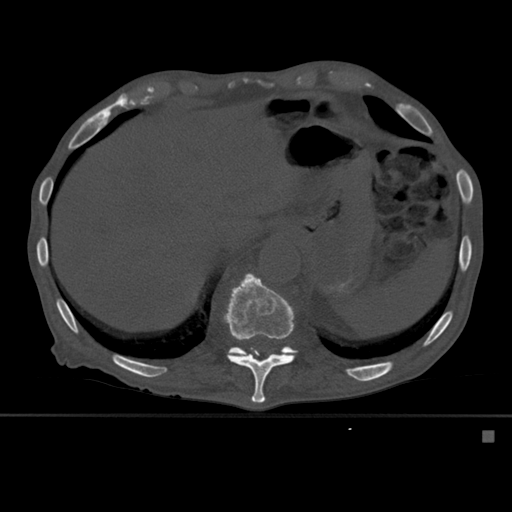
CT including the spine, one axial slice. Position 291 of 527 along the scan axis. Bone window (W 1800 / L 400 HU). 512 × 512 image matrix, field of view 373 × 373 mm. Patient: male, 78 years. Case-level facts recorded for this patient, not image findings: primary cancer: prostate.
Structures marked on this image (semi-automatically segmented with operator editing):
- T11 vertebra: bounding box [x1, y1, x2, y2] px = [223, 273, 295, 404]
- T12 vertebra: [227, 346, 297, 357]